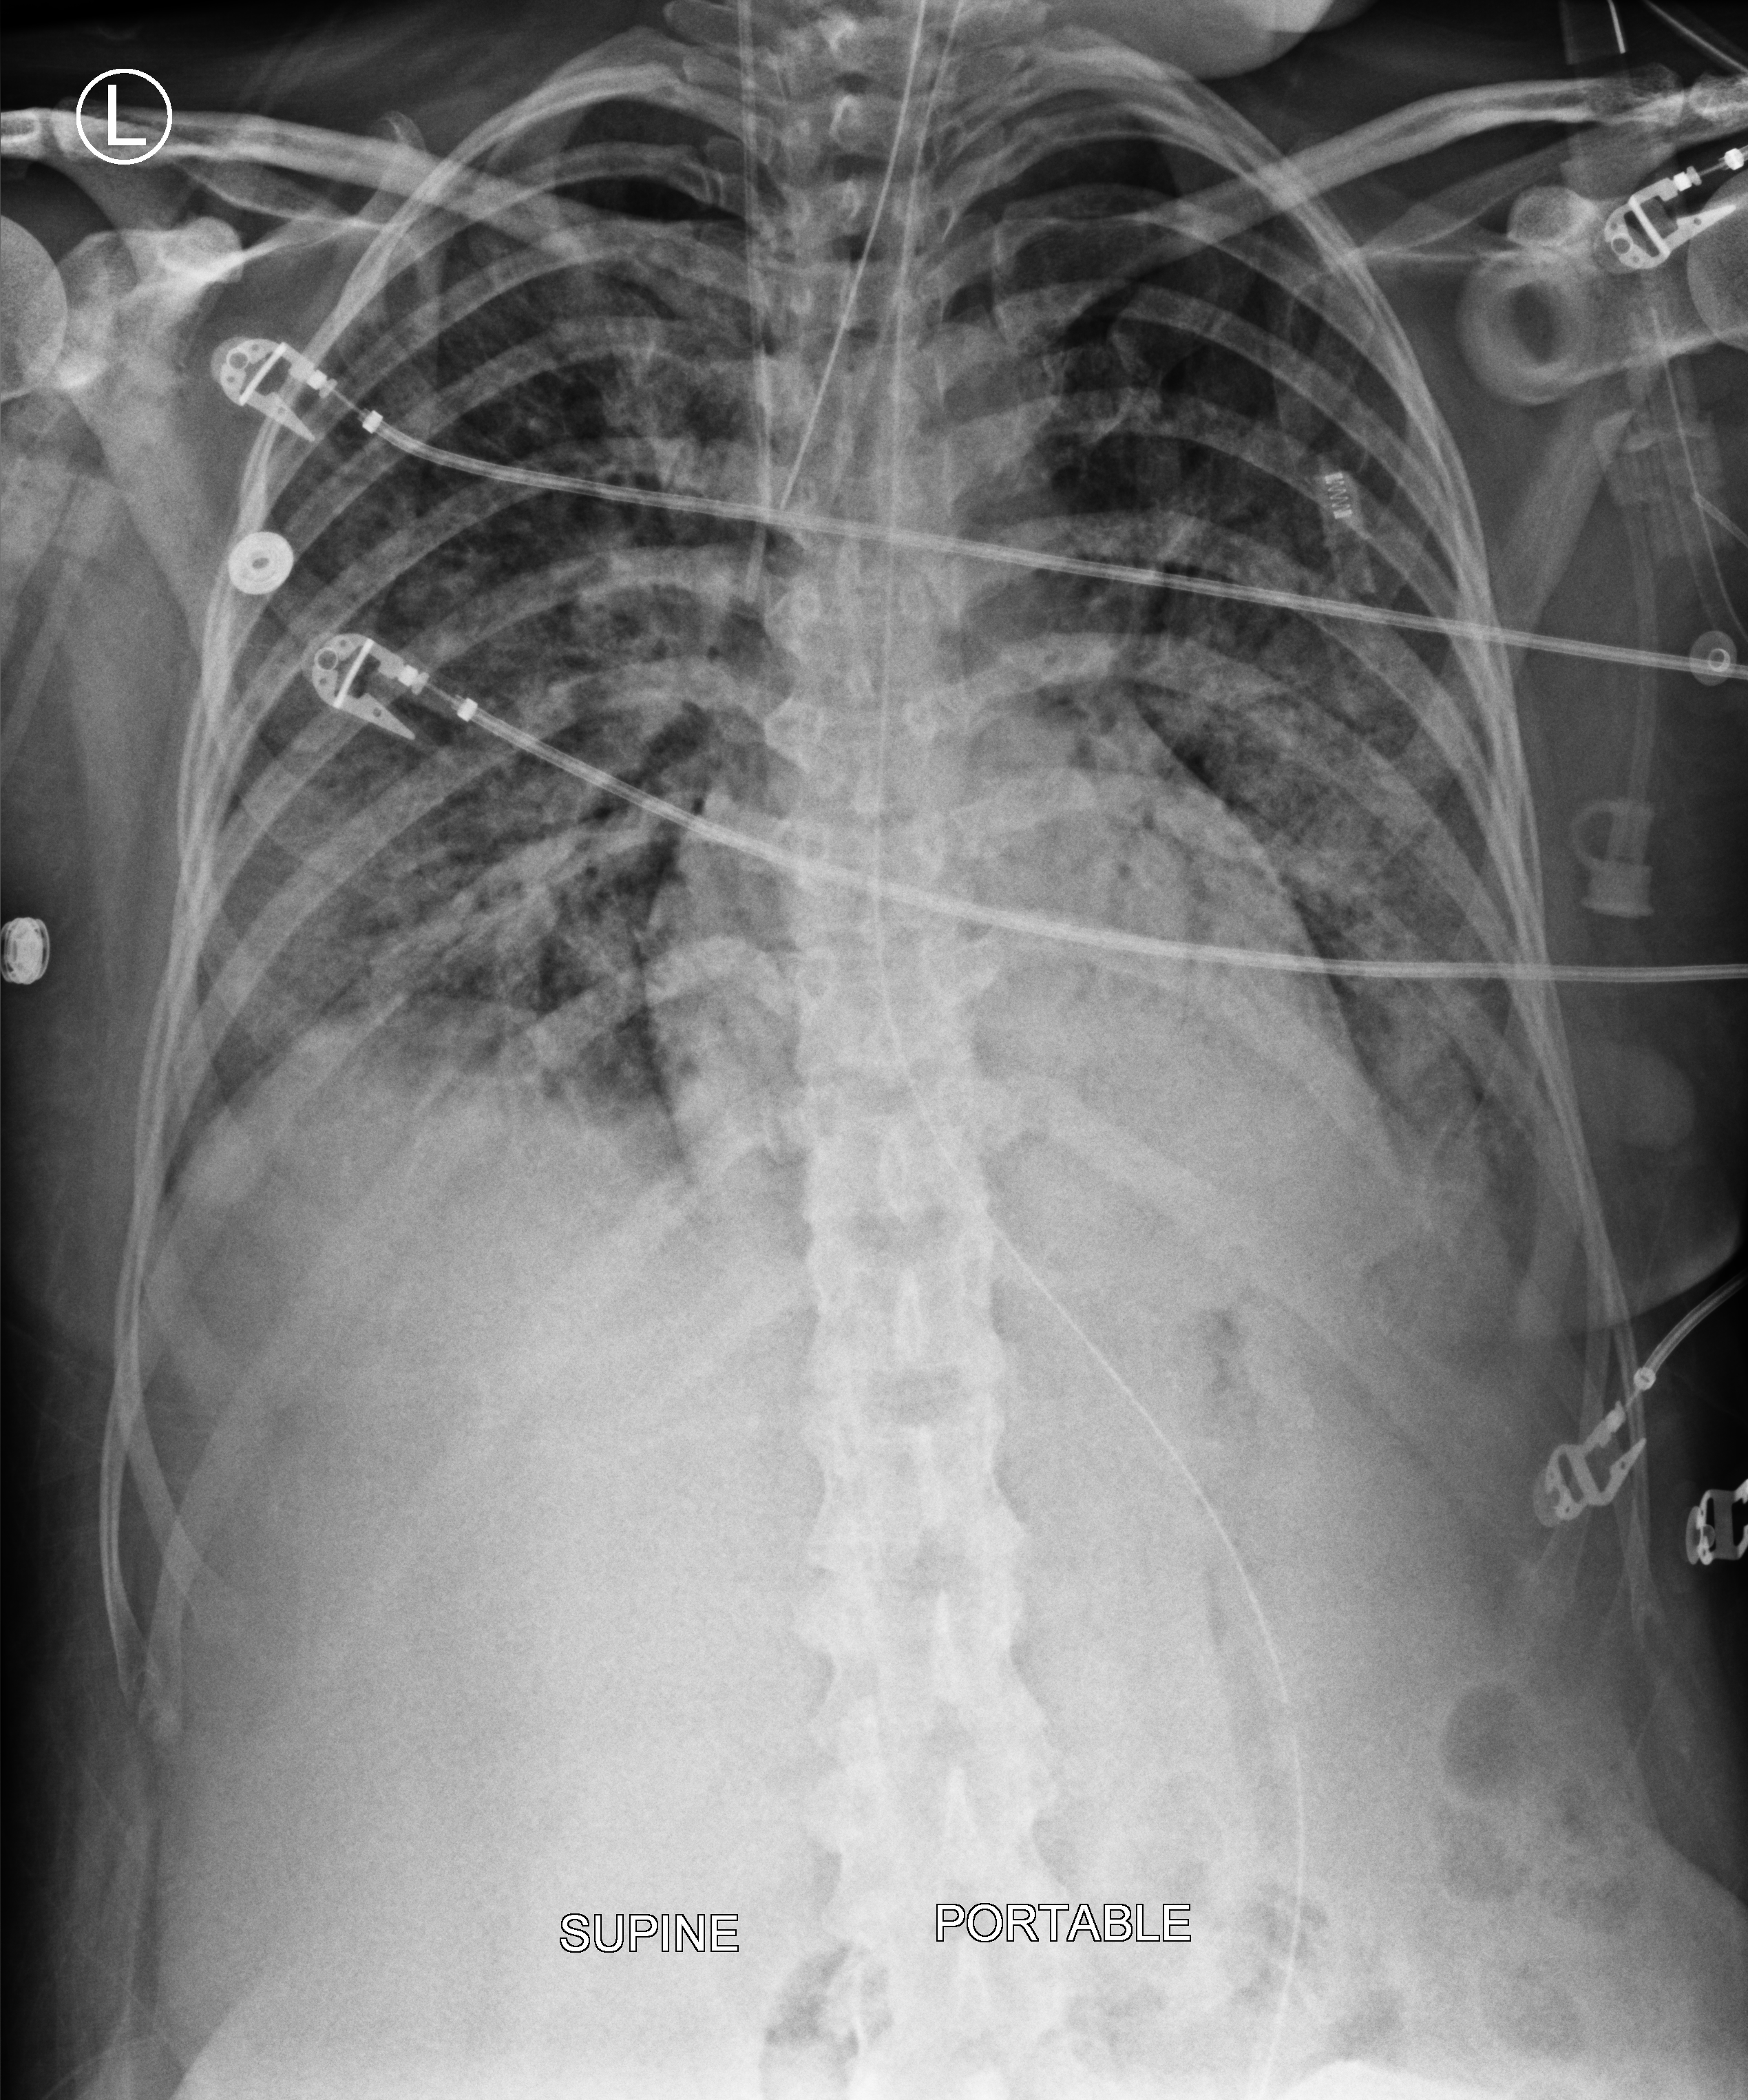
Bedside chest radiograph (computed radiography), anteroposterior (AP) projection. Patient hospitalised with COVID-19; female, aged 18–59 years.
From the hospital-stay record, not from the radiograph (when in the stay this image was taken is not recorded): COPD (admission record): no; length of hospital stay: 71 days; mechanically ventilated during this hospital stay: yes.